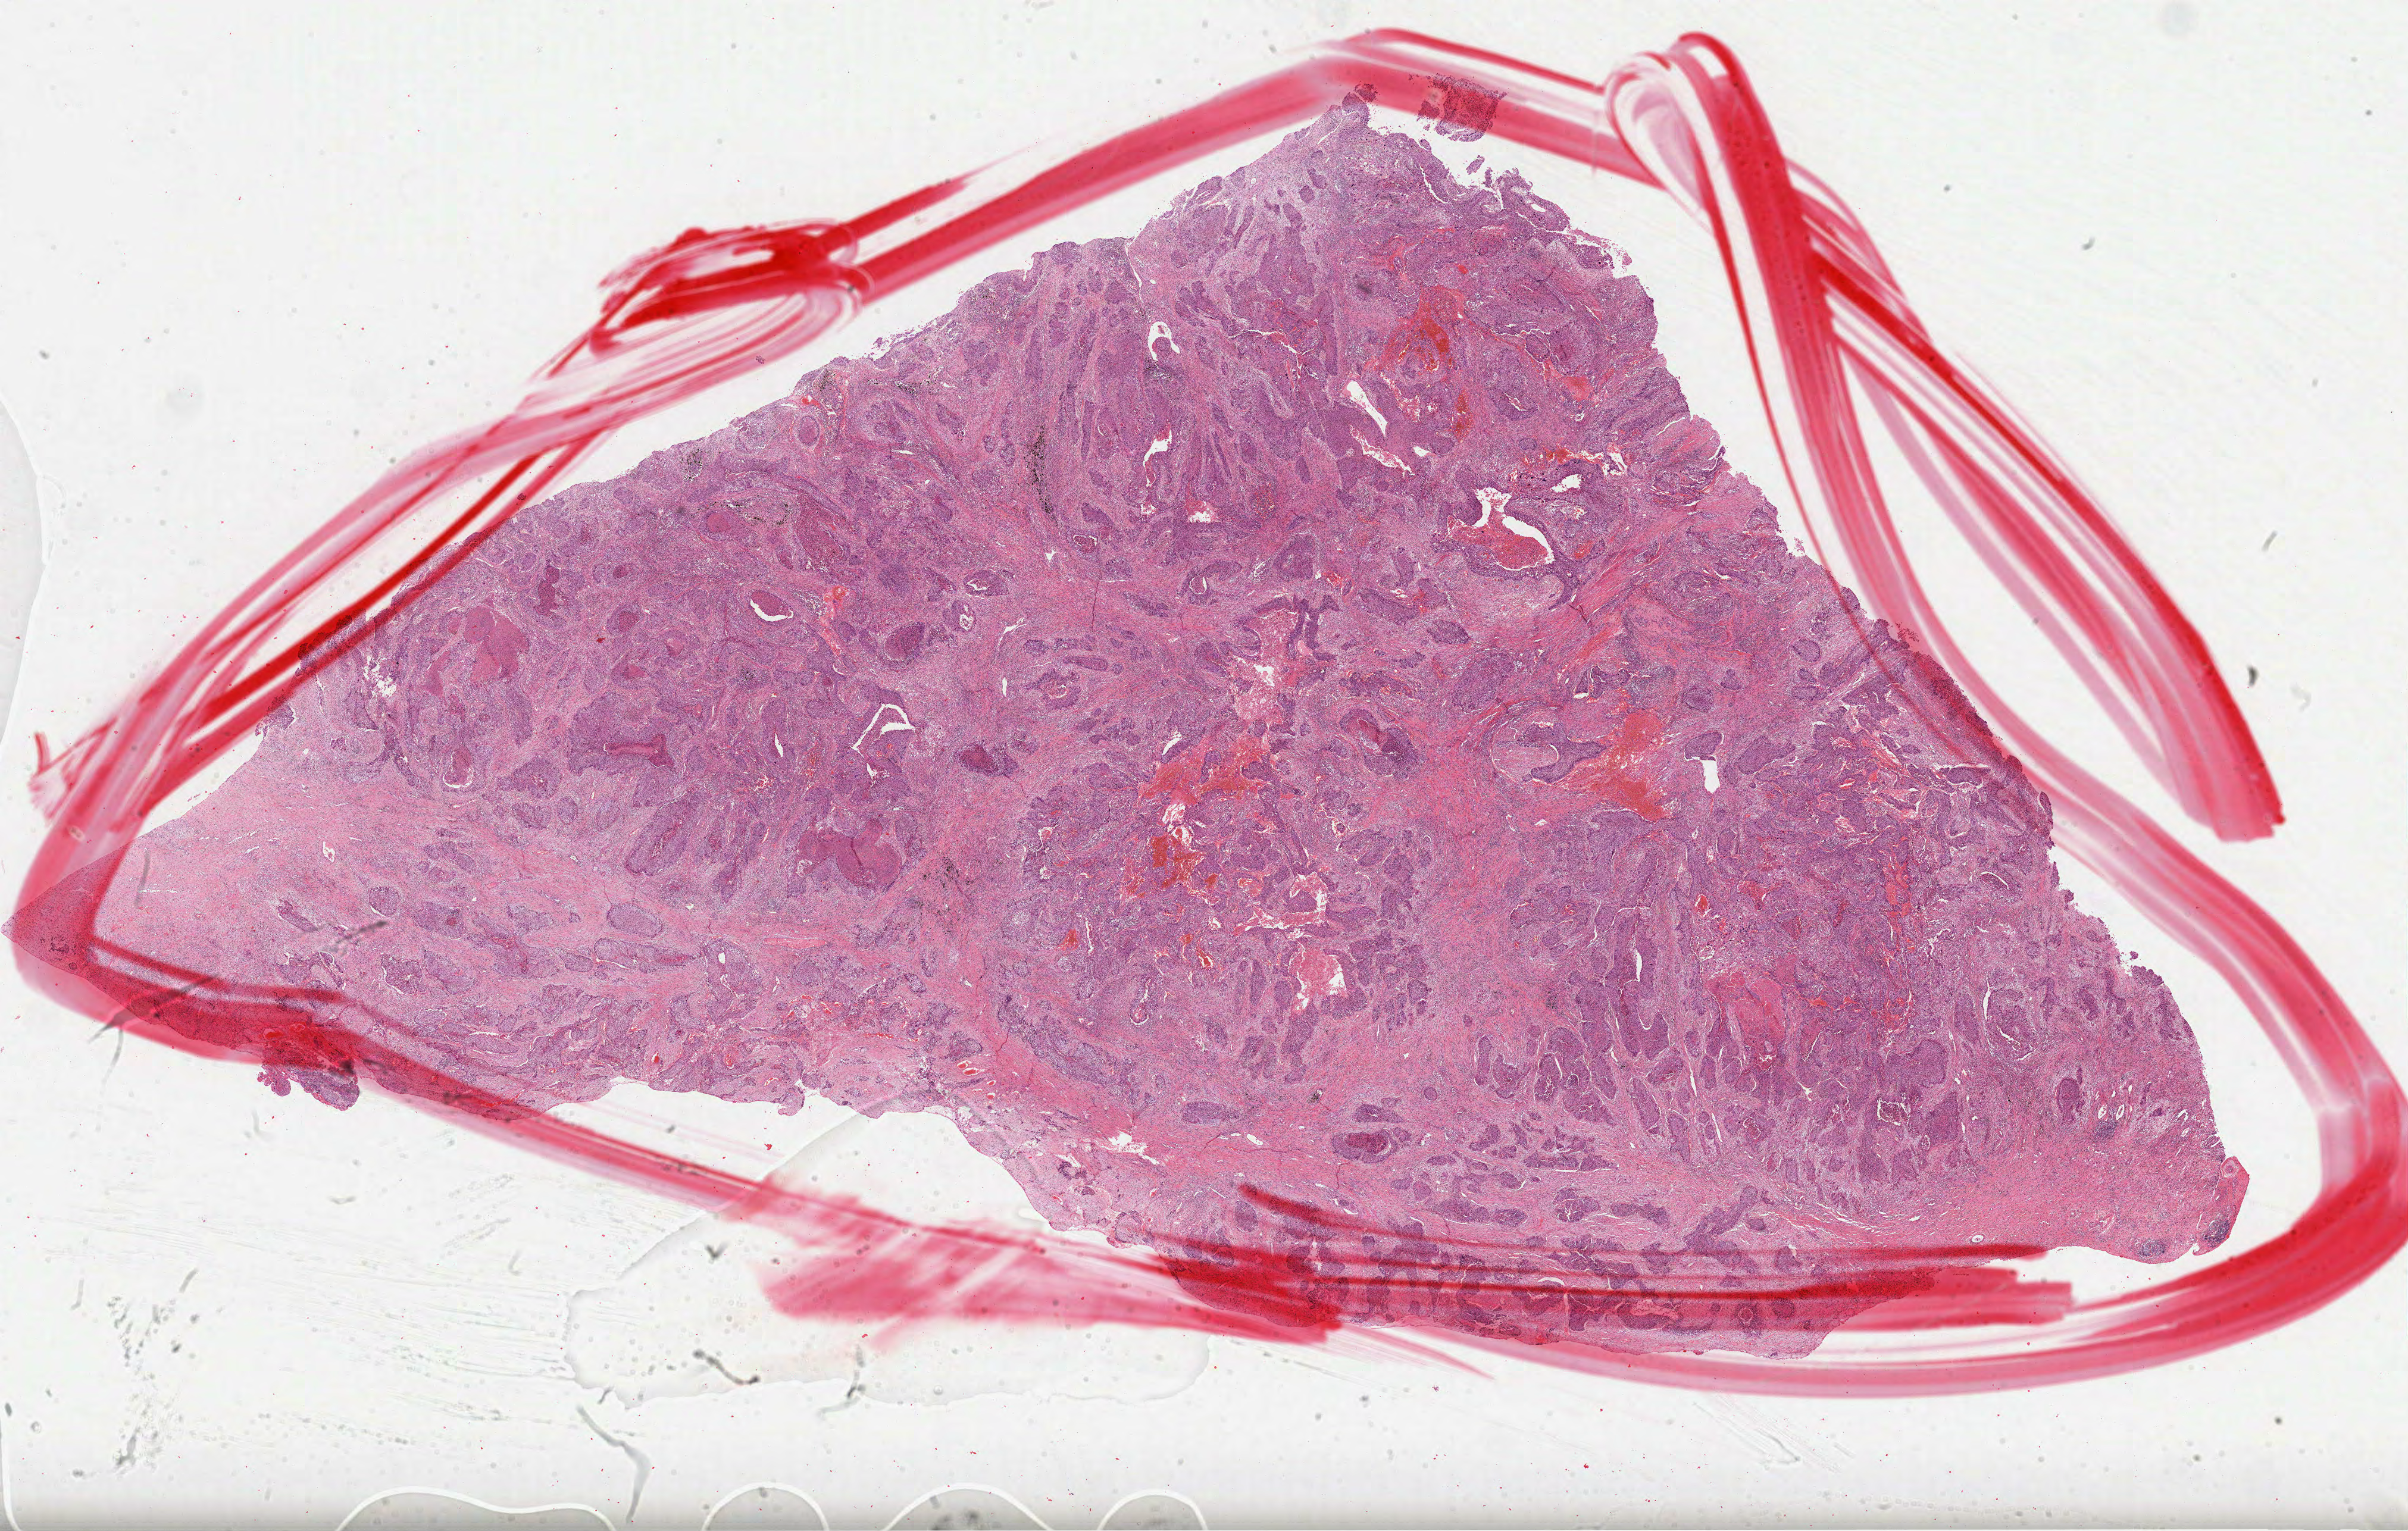
Digitized H&E tissue section (whole slide), a low-resolution overview of the entire scanned area, about 32.6 x 20.8 mm (acquisition: 40x scan). Formalin-fixed paraffin-embedded (FFPE) diagnostic section. Lung, primary tumour sample. Male, age 57 years at initial diagnosis.
- AJCC pathologic stage: IIIA (7th edition)
- pathologic diagnosis: Squamous cell carcinoma, NOS (upper lobe, lung)